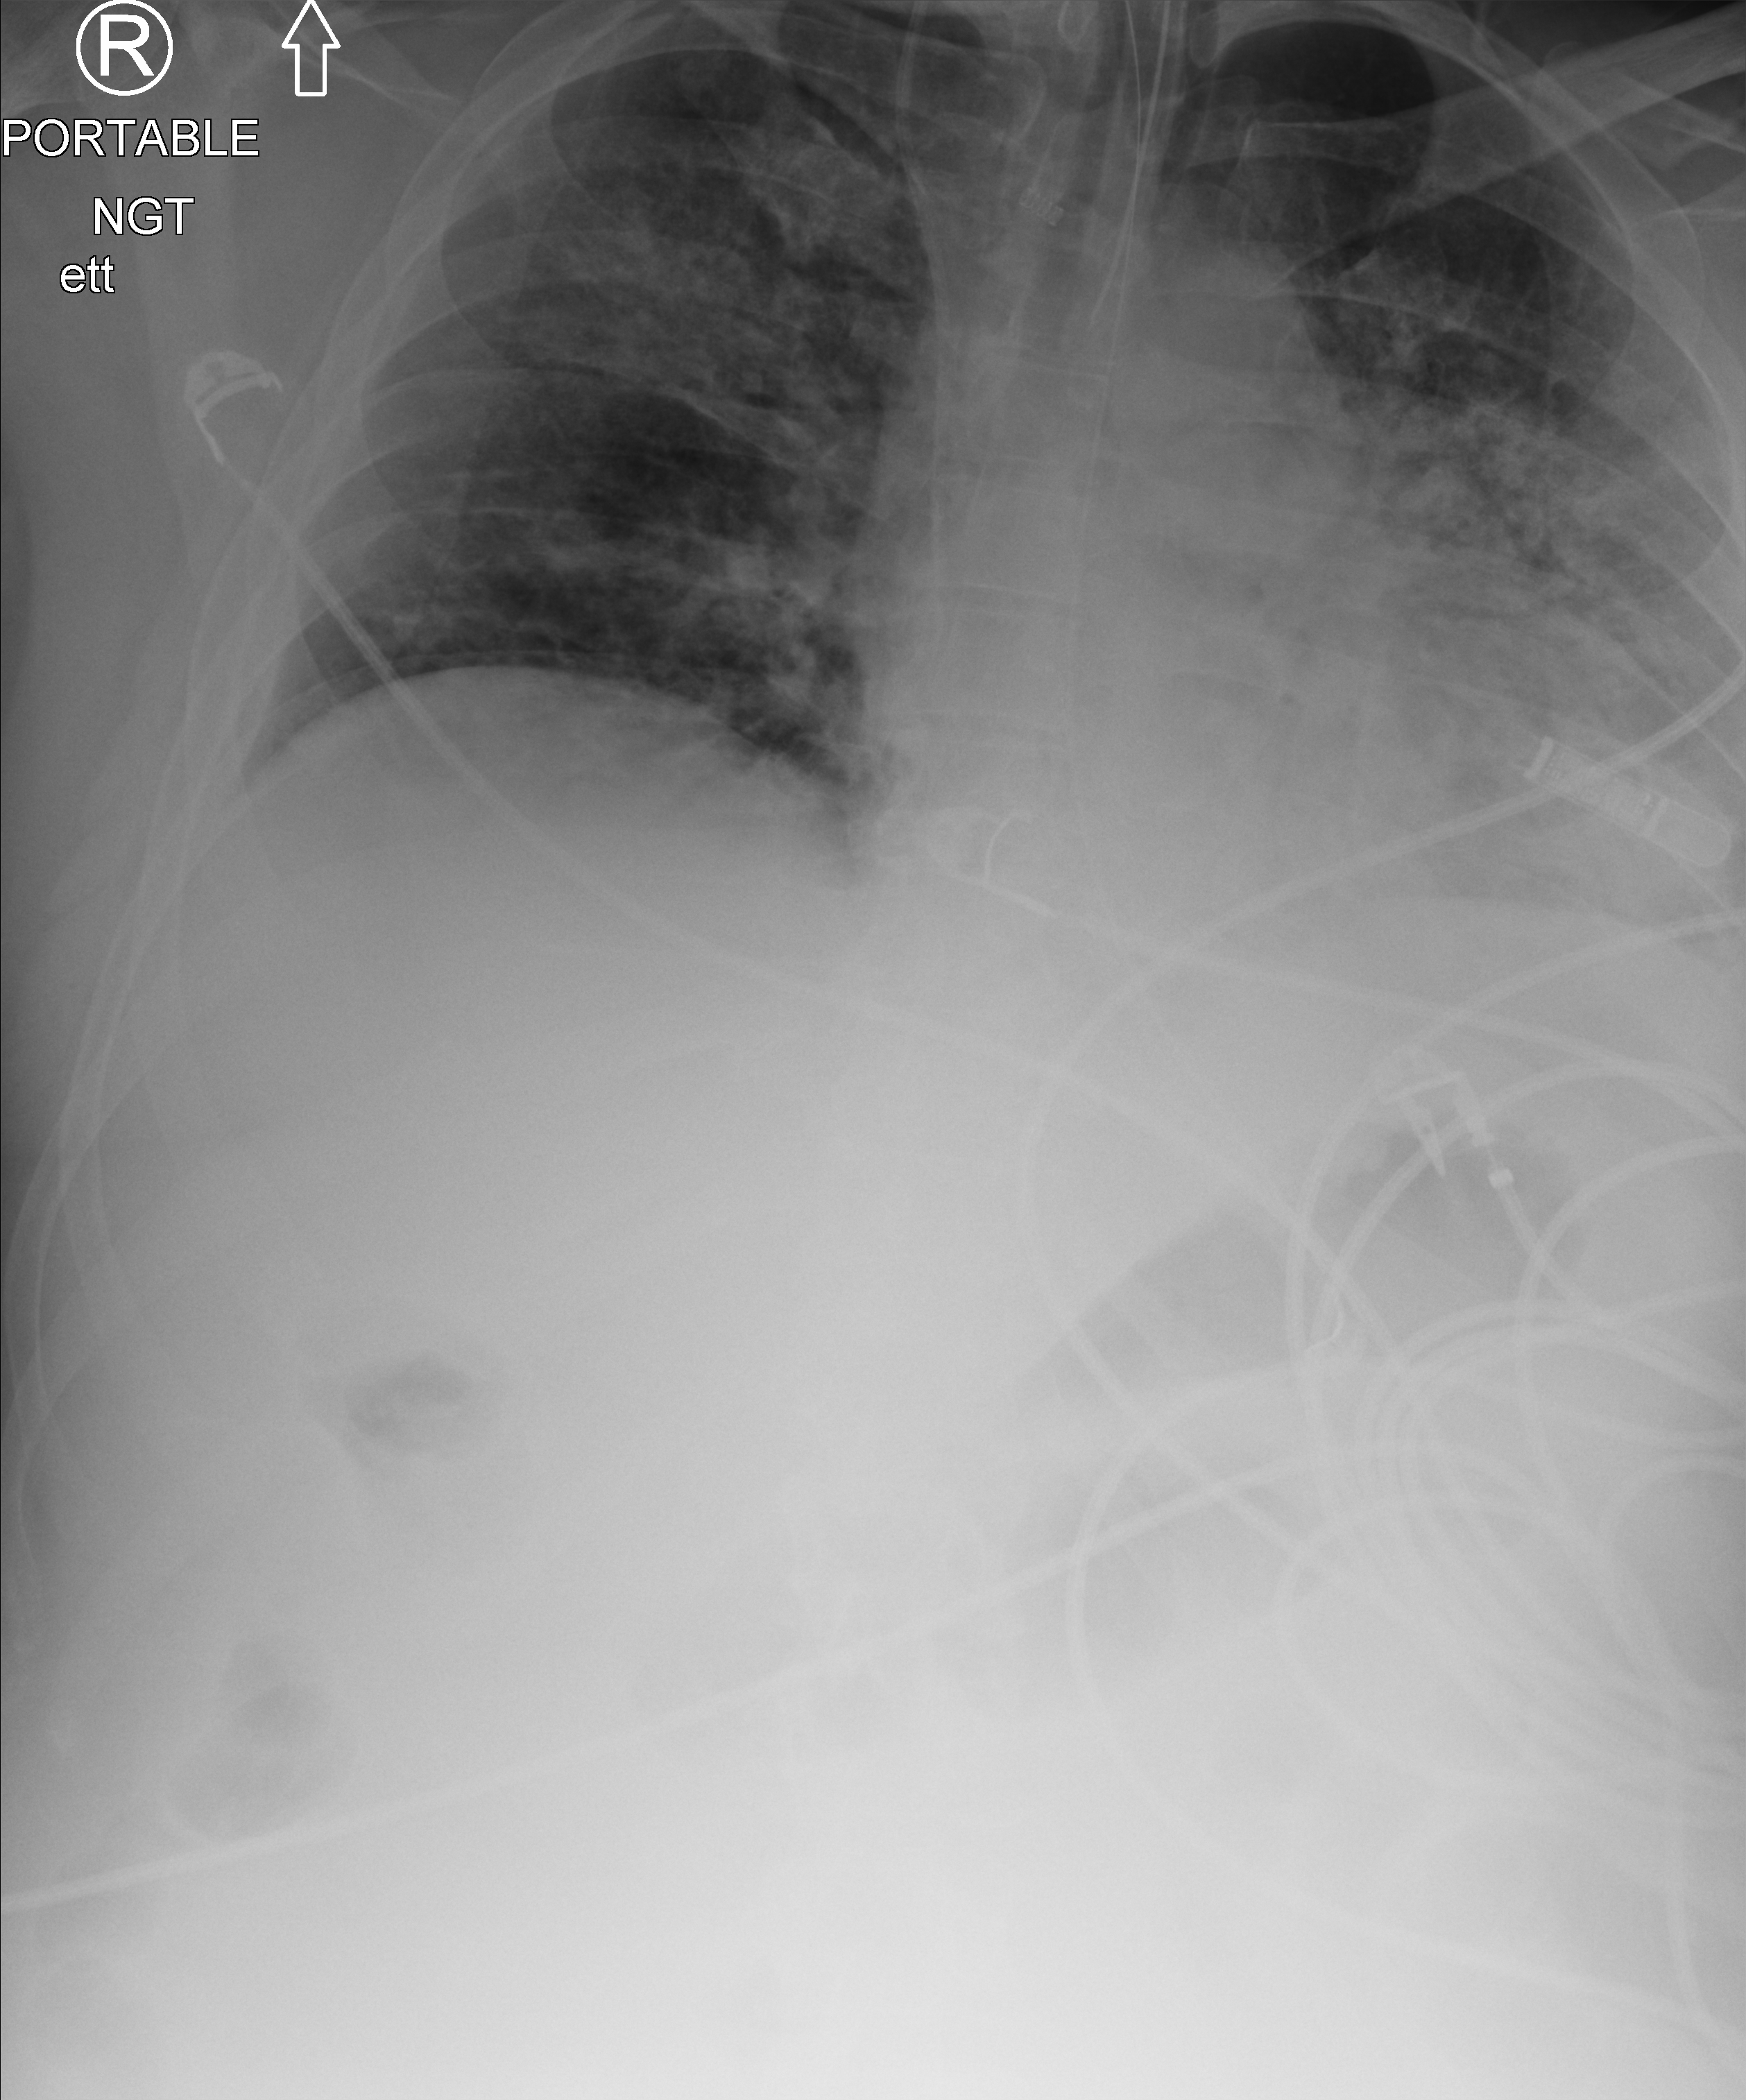
Chest X-ray (portable), anteroposterior (AP) projection. Male patient hospitalised with COVID-19, age 18–59 years.
From the hospital-stay record, not from the radiograph (when in the stay this image was taken is not recorded): mechanically ventilated during this hospital stay: yes.